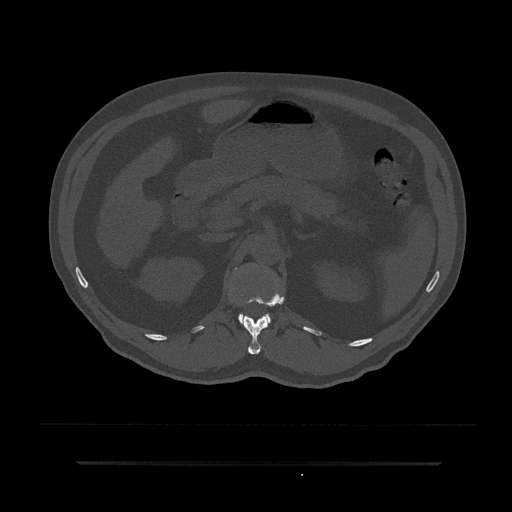
CT including the spine, one axial slice. Slice 184 of 797 in the series (ordered by position). Reconstruction kernel Br40s/3. 120 kVp. Bone window (W 1800 / L 400 HU). 0.5 mm slice thickness. 512 × 512 image matrix, field of view 464 × 464 mm. Patient: male, 59 years. Case-level facts recorded for this patient, not image findings: primary cancer: bile ducts; vertebrae with lytic lesions (as recorded): T10.
Annotated regions visible in this slice (semi-automatically segmented with operator editing):
- L1 vertebra: box from (x=238, y=301) to (x=271, y=322) px
- T12 vertebra: (x=235, y=291)–(x=284, y=355)